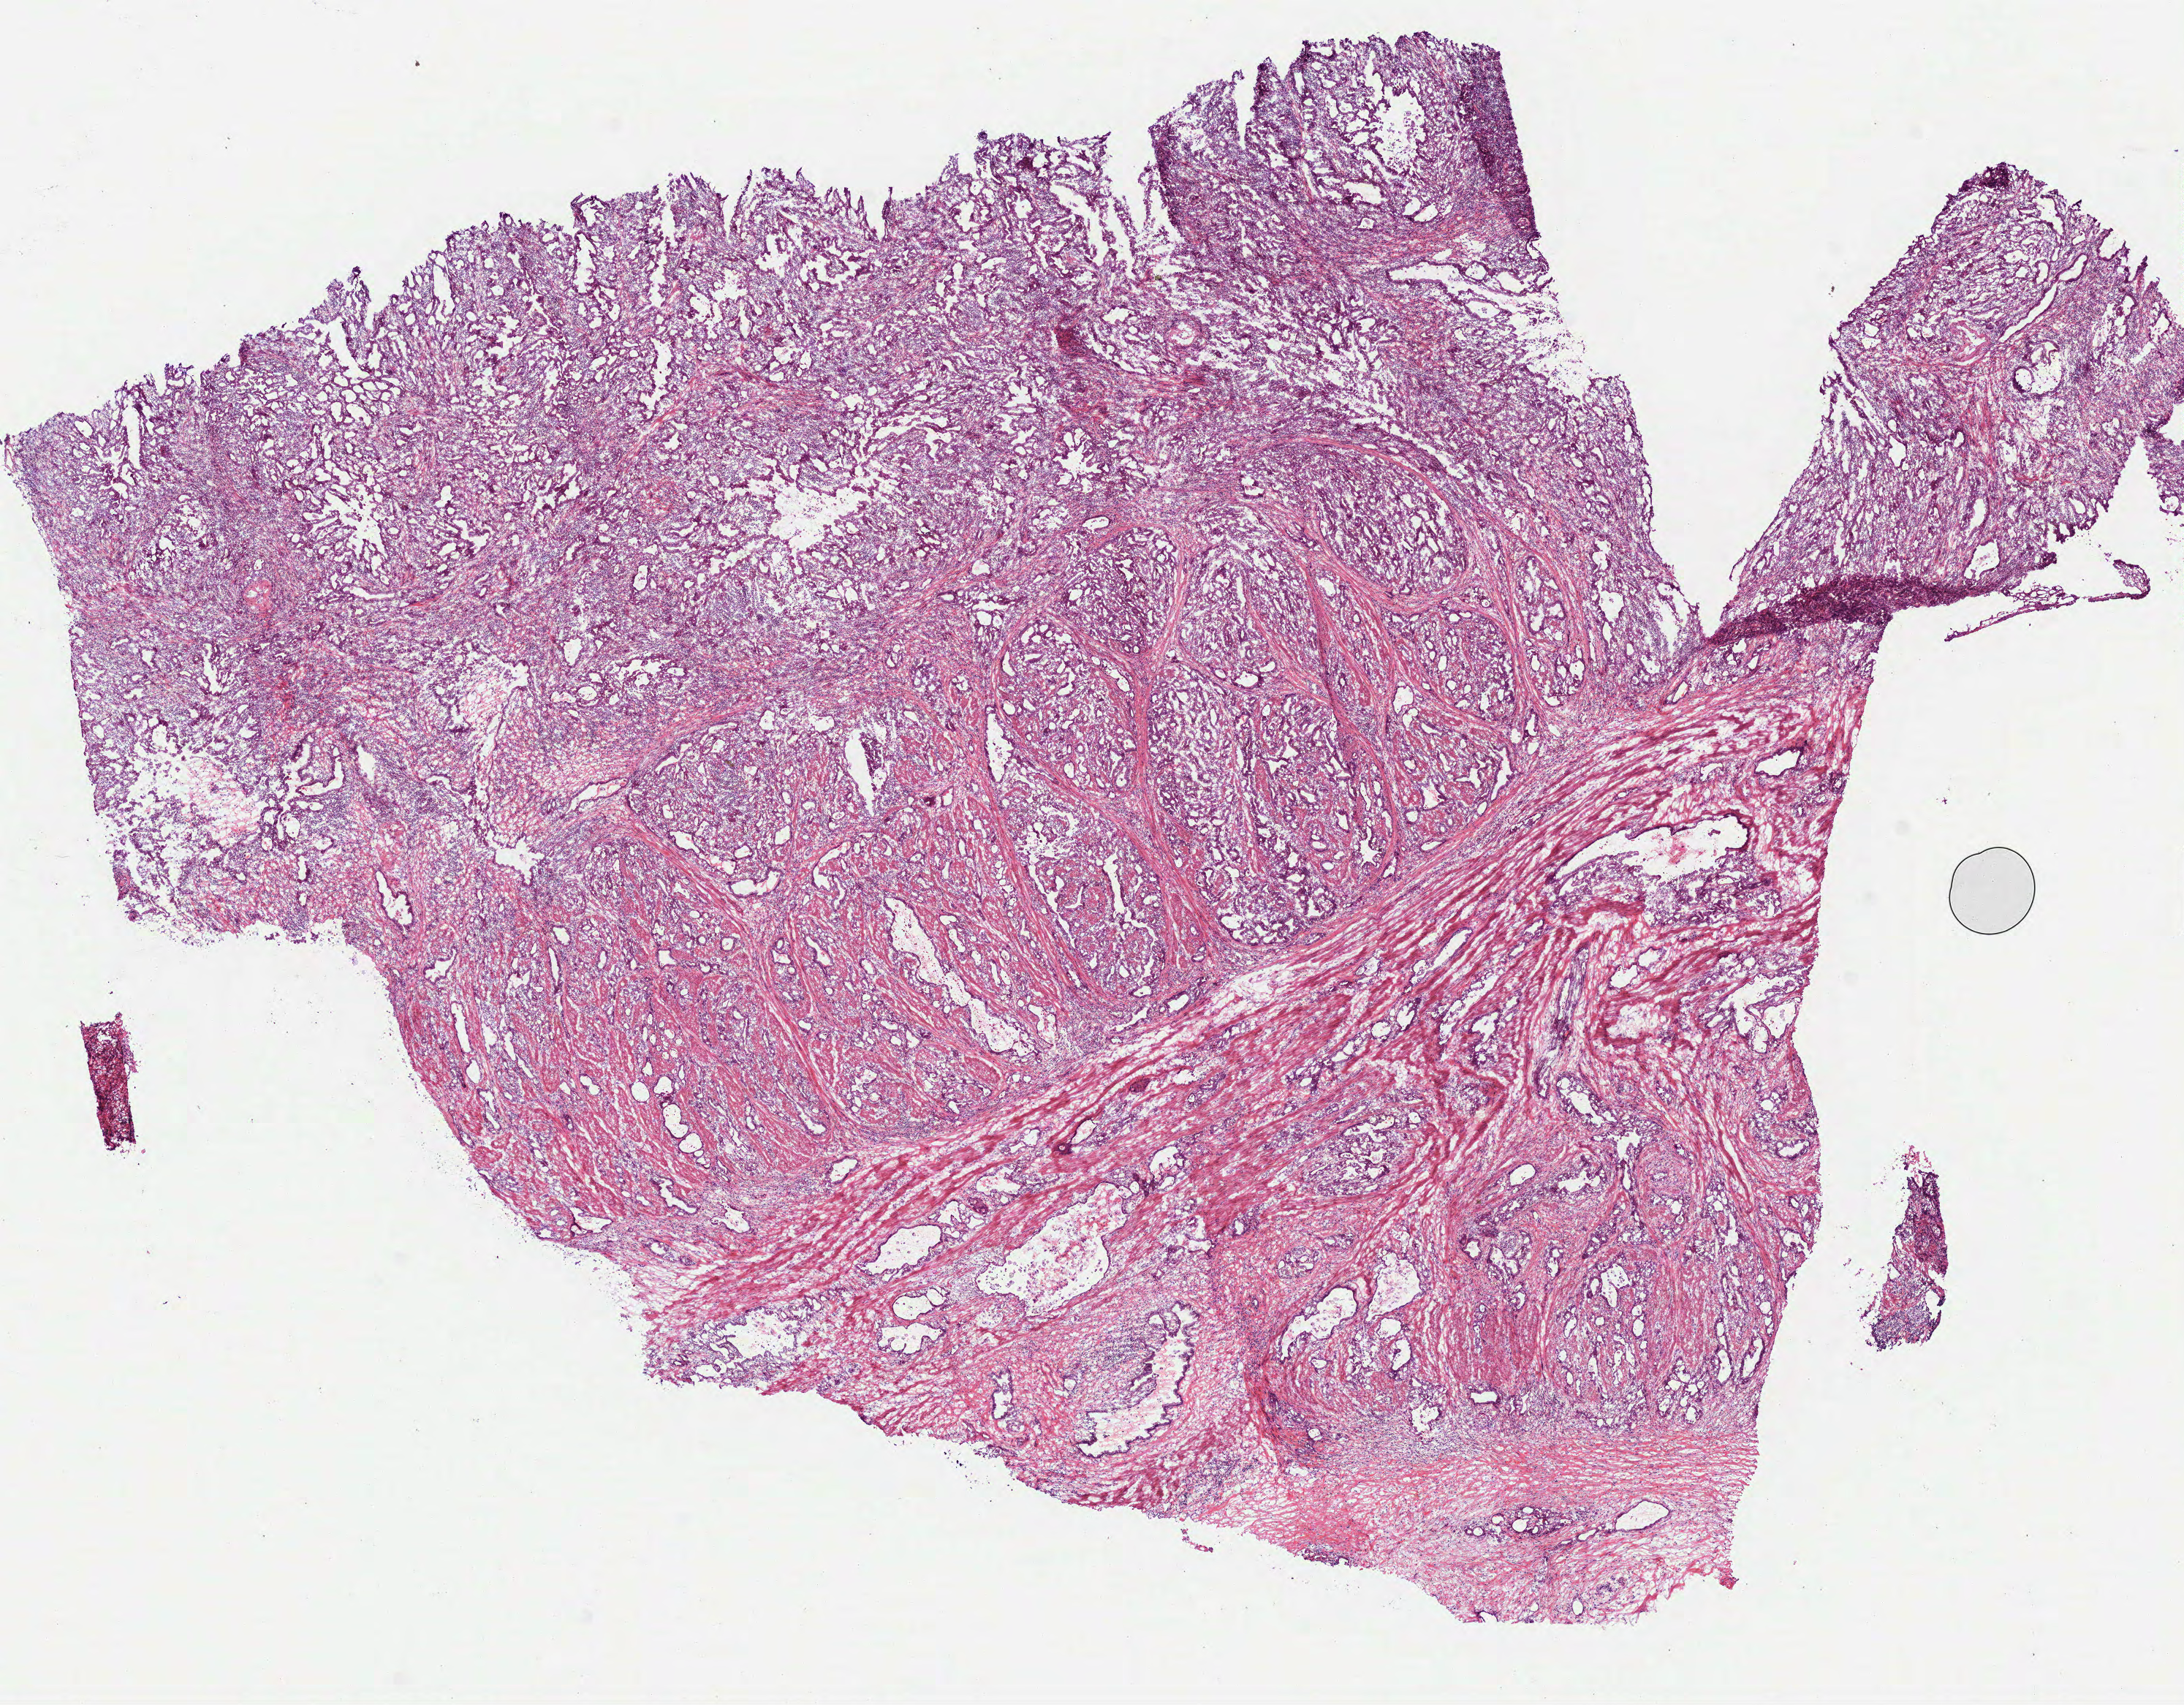
Digitized H&E tissue section (whole slide), low-resolution overview of the scanned area, about 12.0 x 9.4 mm, frozen section from the bottom of the tissue portion, sample: primary tumour, stomach. Male patient; age at initial diagnosis 52 years. Histologic grade: G2 (moderately differentiated). Slide review estimates, as recorded: tumour cells 85%, tumour nuclei 50%, normal cells 0%, stromal cells 15%, necrosis 0%.
AJCC pathologic stage: II. Pathologic diagnosis: Adenocarcinoma, NOS. TNM: T3 N0 M0.